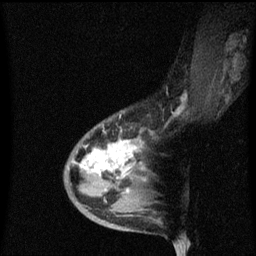
Breast MRI (dynamic contrast-enhanced), one sagittal slice; position 27 of 60 along the scan axis; dynamic contrast-enhanced series, image 2 of 3 at this slice position (ordered by acquisition); 1.5 T; TE 4.2 ms, TR 8.4 ms; 256 × 256 image matrix, field of view 200 × 200 mm. Female patient, age 38 years. From the clinical record (not read from this slice): setting: breast cancer imaged before/during neoadjuvant chemotherapy; receptor status: HR-positive, HER2-negative.
Outlined on this slice (semi-automatic segmentation, software-assisted and operator-edited):
- analysis volume of interest (the breast-tissue region the enhancement analysis was run in; not a lesion): bounding box <64,114,151,205> (left, top, right, bottom; pixels)
- tumour enhancement mask (voxels above the 70 % enhancement threshold inside the analysis volume of interest): <80,140,135,175>